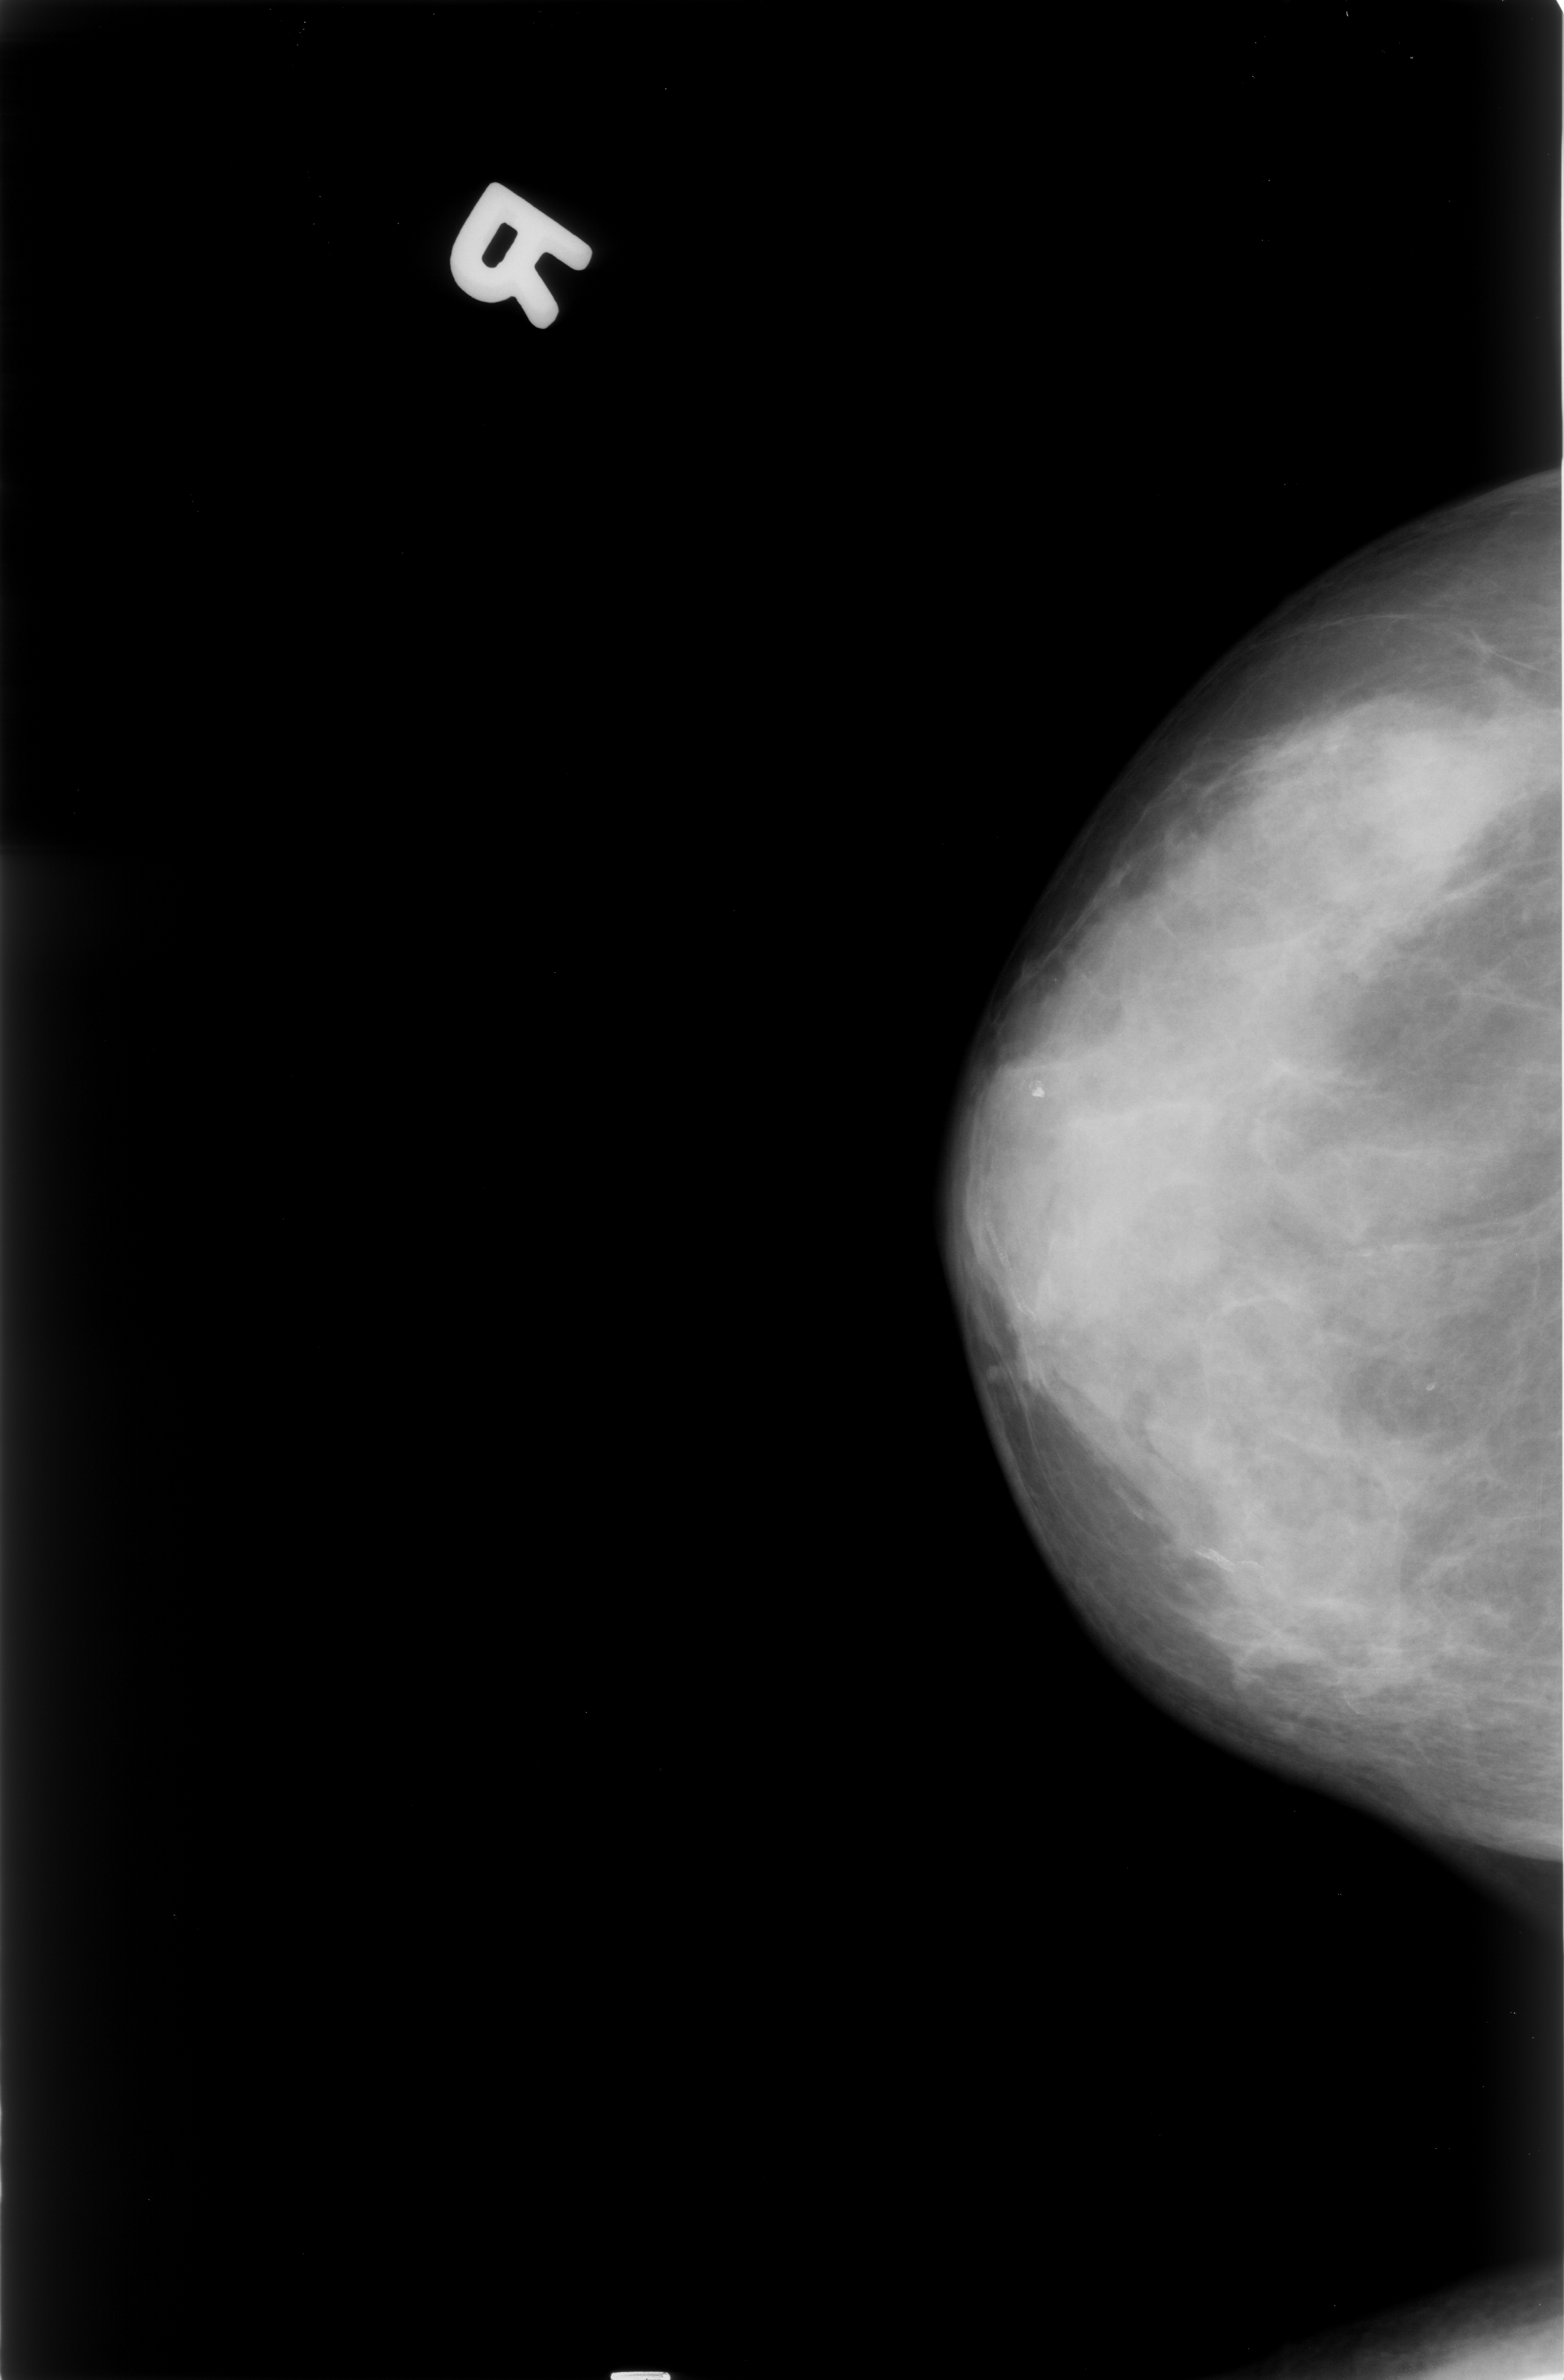
Mammogram (digitized film); right breast; craniocaudal (CC) view; BI-RADS breast density category 4 (scale 1–4); 1564 × 2380 image matrix.
Marked abnormalities (boxes around the expert regions of interest):
- mass, shape irregular, margins obscured; BI-RADS assessment category 4; subtlety rating 3 on a 1 (subtle) to 5 (obvious) scale; pathology result (as recorded, not read from the image): malignant: bounding box [x1, y1, x2, y2] px = [1352, 727, 1507, 855]